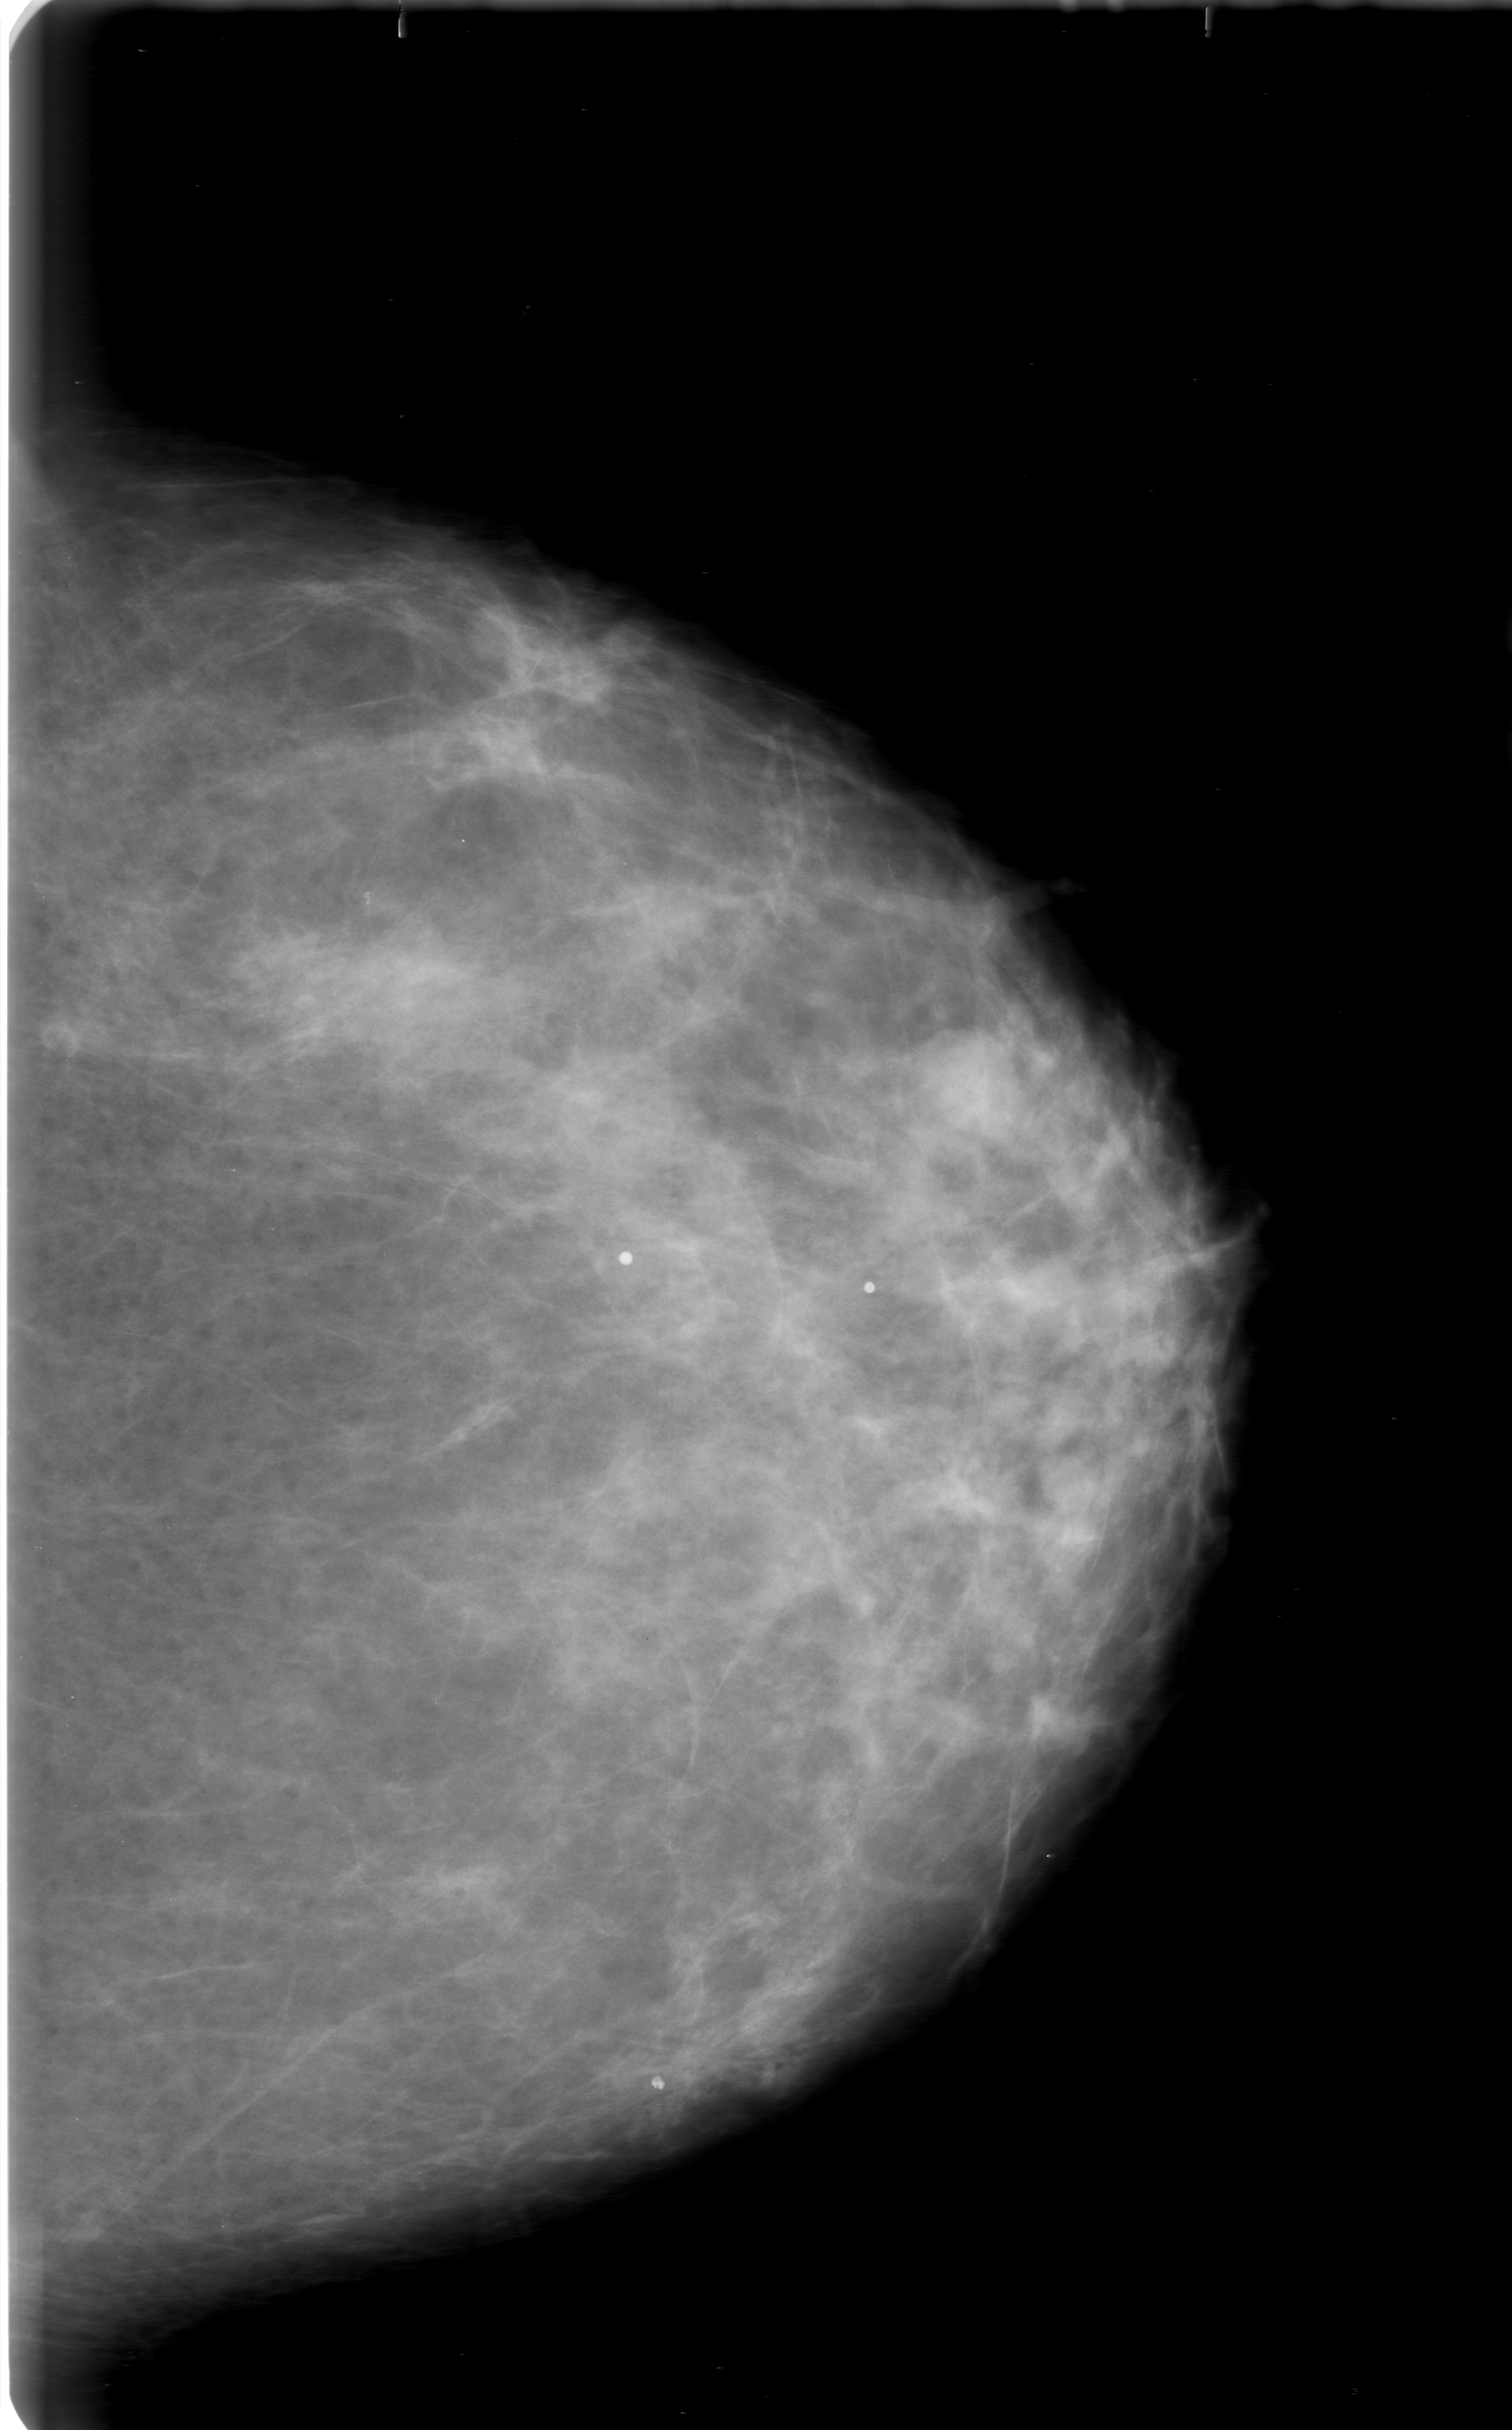
Mammogram (digitized film), left breast, craniocaudal (CC) view, breast composition: scattered fibroglandular densities (BI-RADS density category 2 of 4).
Marked abnormality: mass, shape oval, margins obscured; BI-RADS assessment category 0; subtlety rating 3 on a 1 (subtle) to 5 (obvious) scale; pathology (as recorded): benign.